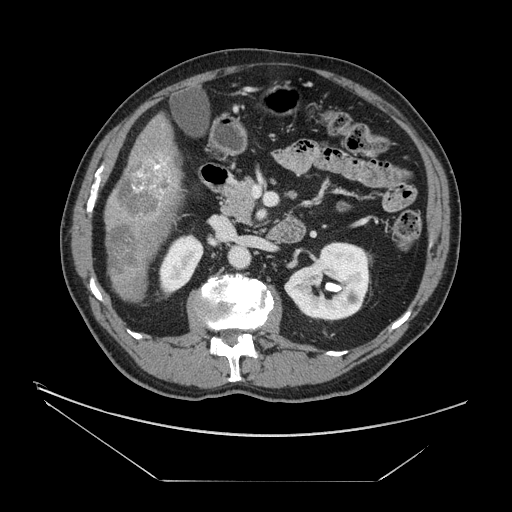
Contrast-enhanced abdominal CT, one axial slice. Slice 64 of 161 in the series (ordered by position). Reconstruction kernel STANDARD. 120 kVp. Intravenous contrast given. Soft-tissue window (W 400 / L 40 HU). 512 × 512 image matrix. Male patient, age 65 years. From the clinical record (not read from this slice): diagnosis: colorectal cancer liver metastases, imaged before liver resection; multiple liver metastases: yes; largest metastasis: 4.2 cm.
Annotated regions visible in this slice (expert manual segmentation):
- liver: bounding box (x1, y1, x2, y2) in pixels: (105, 116, 184, 302)
- portal vein (with intrahepatic branches): (134, 158, 170, 199)
- liver metastasis: (108, 226, 139, 276)
- liver metastasis: (116, 159, 172, 222)